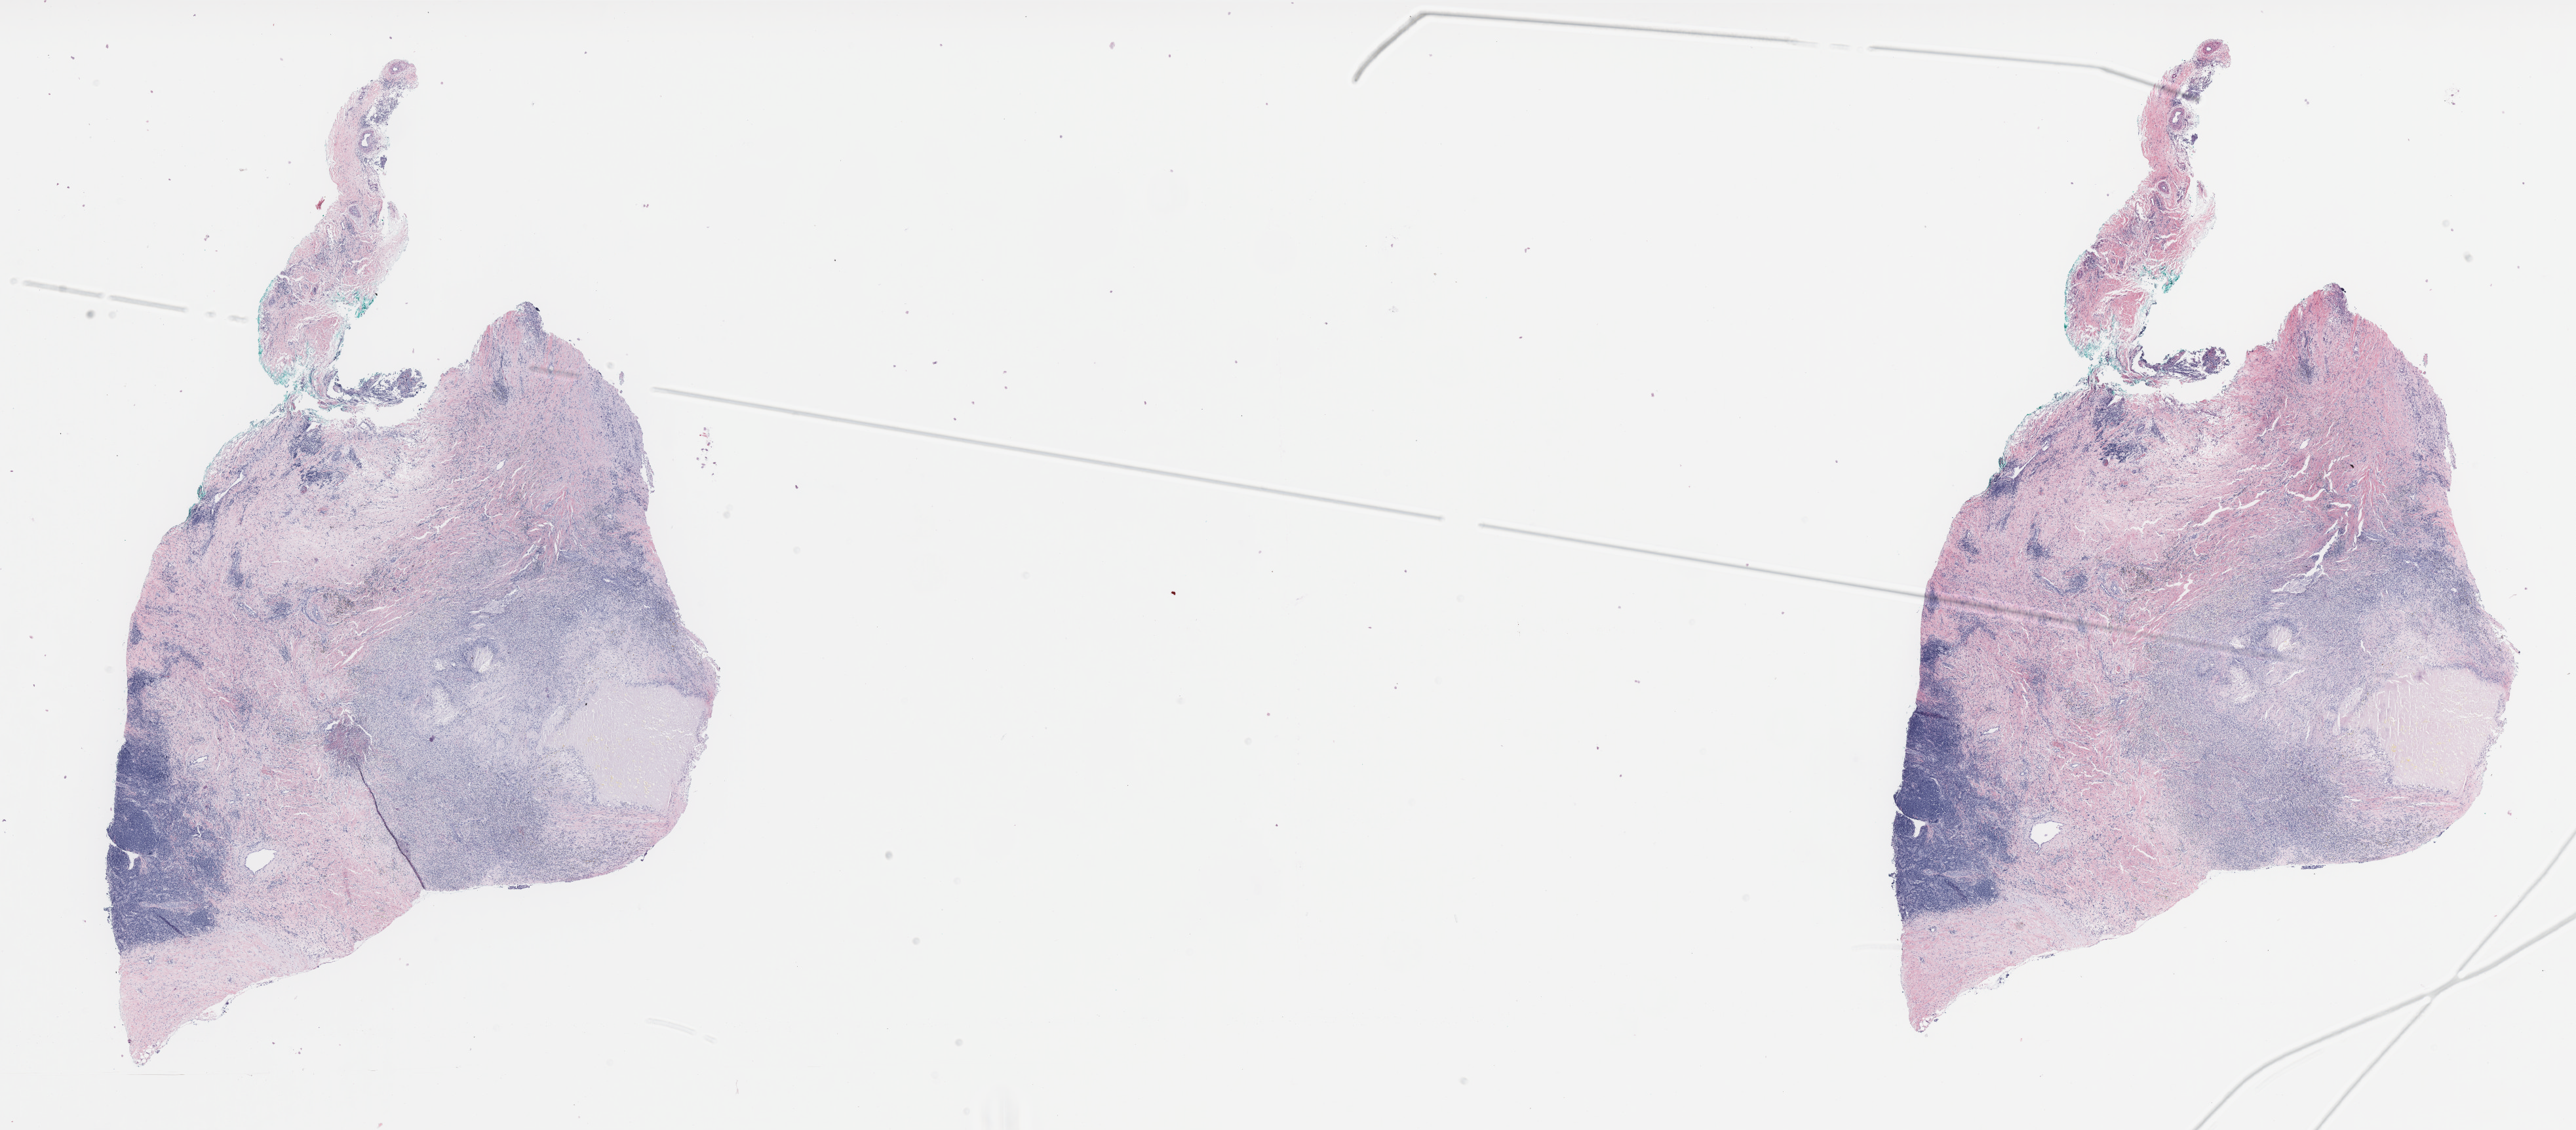
Whole-slide histology image, H&E, low-resolution overview of the scanned area, about 31.5 x 13.8 mm (from a 40x scan). Formalin-fixed paraffin-embedded (FFPE) diagnostic section. Sample: primary tumour, skin. Patient: female, age at initial diagnosis 75 years.
Diagnosis: Malignant melanoma, NOS.